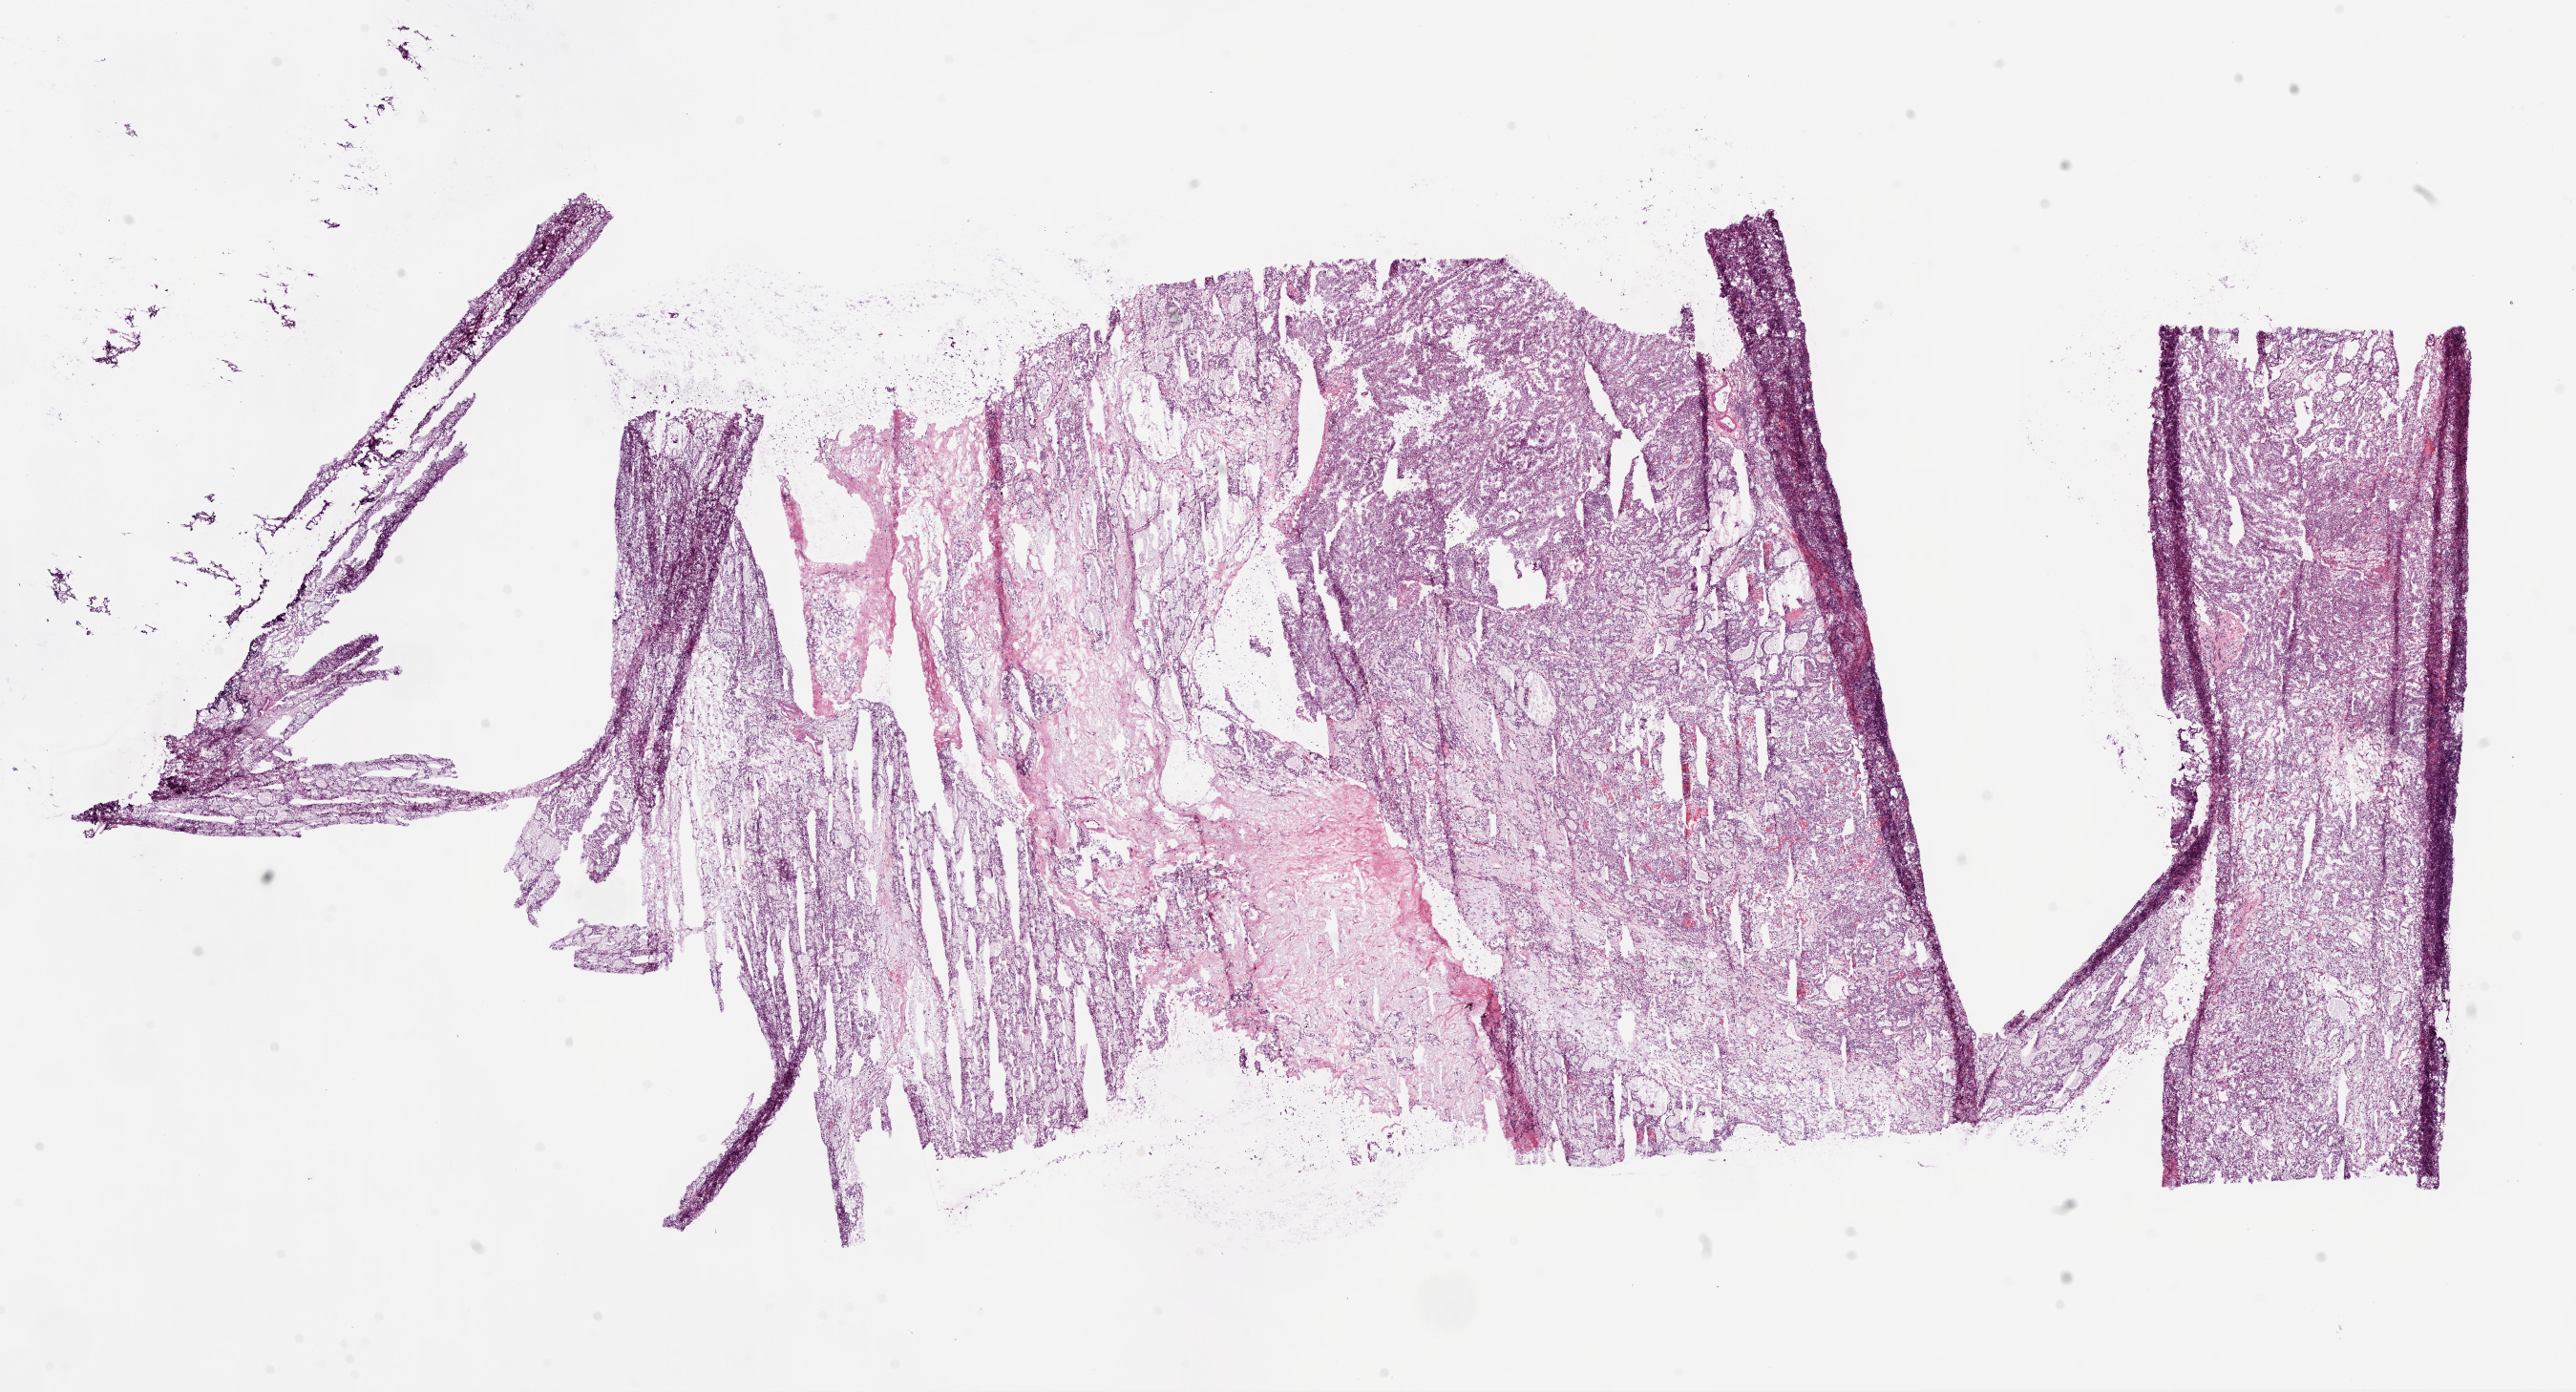
Whole-slide histology image, H&E, a low-resolution overview of the entire scanned area, about 21.8 x 11.8 mm (slide scanned at 20x). Frozen section from the bottom of the tissue portion. Sample: primary tumour, kidney. Male patient. Histologic grade: G3 (poorly differentiated). Composition of this section per pathologist review: tumour cells 90%, tumour nuclei 80%, normal cells 0%, stromal cells 10%, necrosis 0%.
- AJCC pathologic stage: I
- TNM: T1a NX M0
- diagnosis: Clear cell adenocarcinoma, NOS
- laterality: left